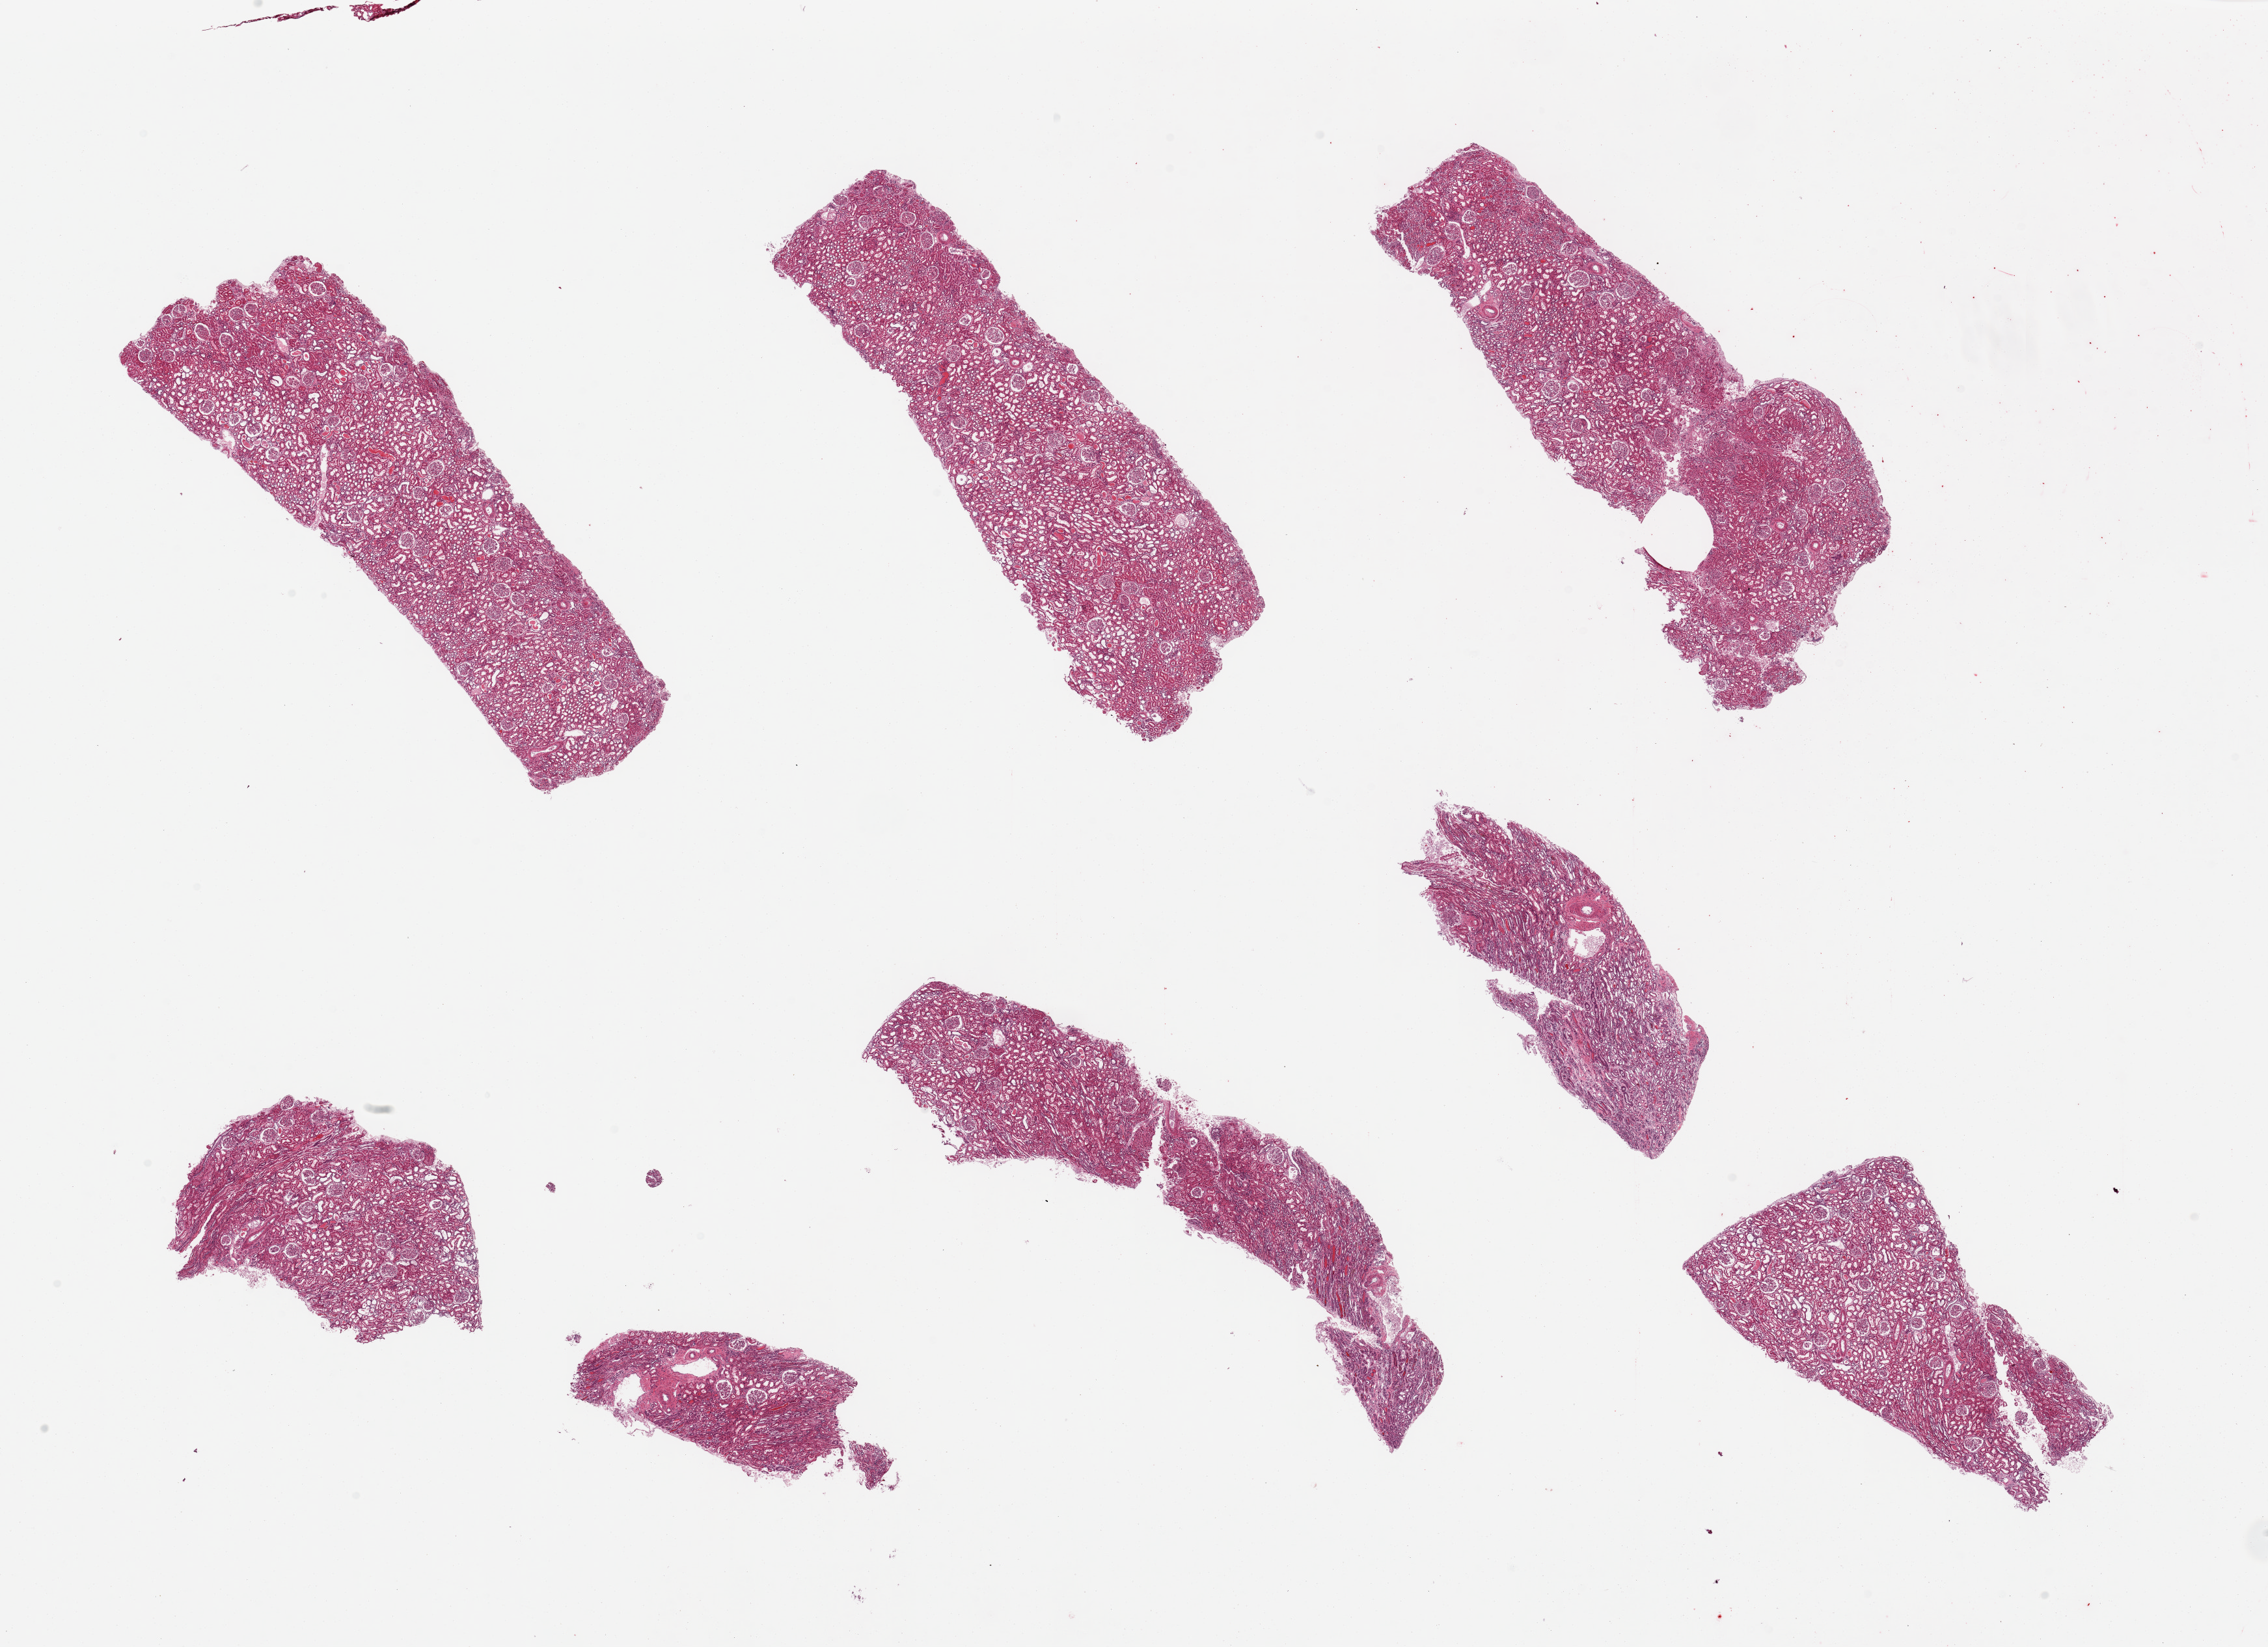
Hematoxylin and eosin (H&E) whole-slide image, low-resolution overview of the scanned area, about 27.6 x 20.0 mm (from a 20x scan), PAXgene-fixed, paraffin-embedded tissue, section of renal cortex (target tissue), tissue donor sample. Donor: male.
* review note (as recorded): 6 pieces; no lesions; medulla in 2 small fragments